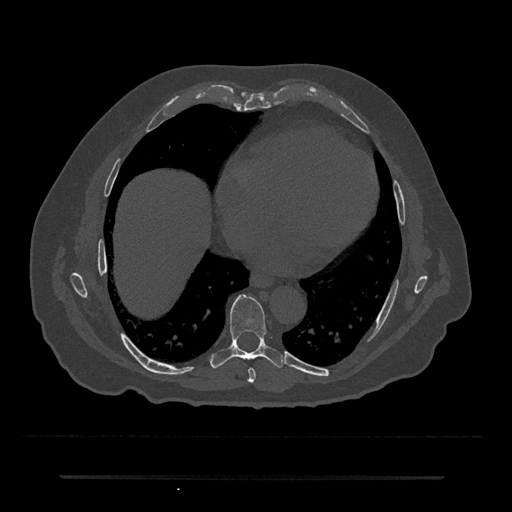
CT including the spine, one axial slice. Position 339 of 797 along the scan axis. Reconstruction kernel Br40s/3. 120 kVp. Bone window (W 1800 / L 400 HU). 0.5 mm slice thickness. 512 × 512 image matrix, field of view 437 × 437 mm. Male patient, age 69 years. From the clinical record (not read from this slice): primary cancer: prostate.
Annotated regions visible in this slice (semi-automatically segmented with operator editing):
- T7 vertebra: bounding box [x1, y1, x2, y2] px = [248, 368, 256, 383]
- T8 vertebra: [211, 294, 283, 368]